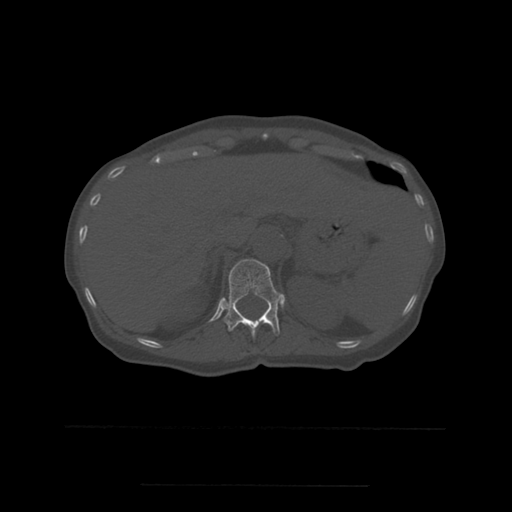
CT including the spine, one axial slice. Slice 261 of 544 in the series (ordered by position). Bone window (W 1800 / L 400 HU). 1.25 mm slice thickness. 512 × 512 image matrix, field of view 350 × 350 mm. Patient age 58 years. From the clinical record (not read from this slice): primary cancer: lung.
Outlined on this slice (semi-automatically segmented with operator editing):
- T12 vertebra: bounding box (x1, y1, x2, y2) in pixels: (224, 259, 284, 338)